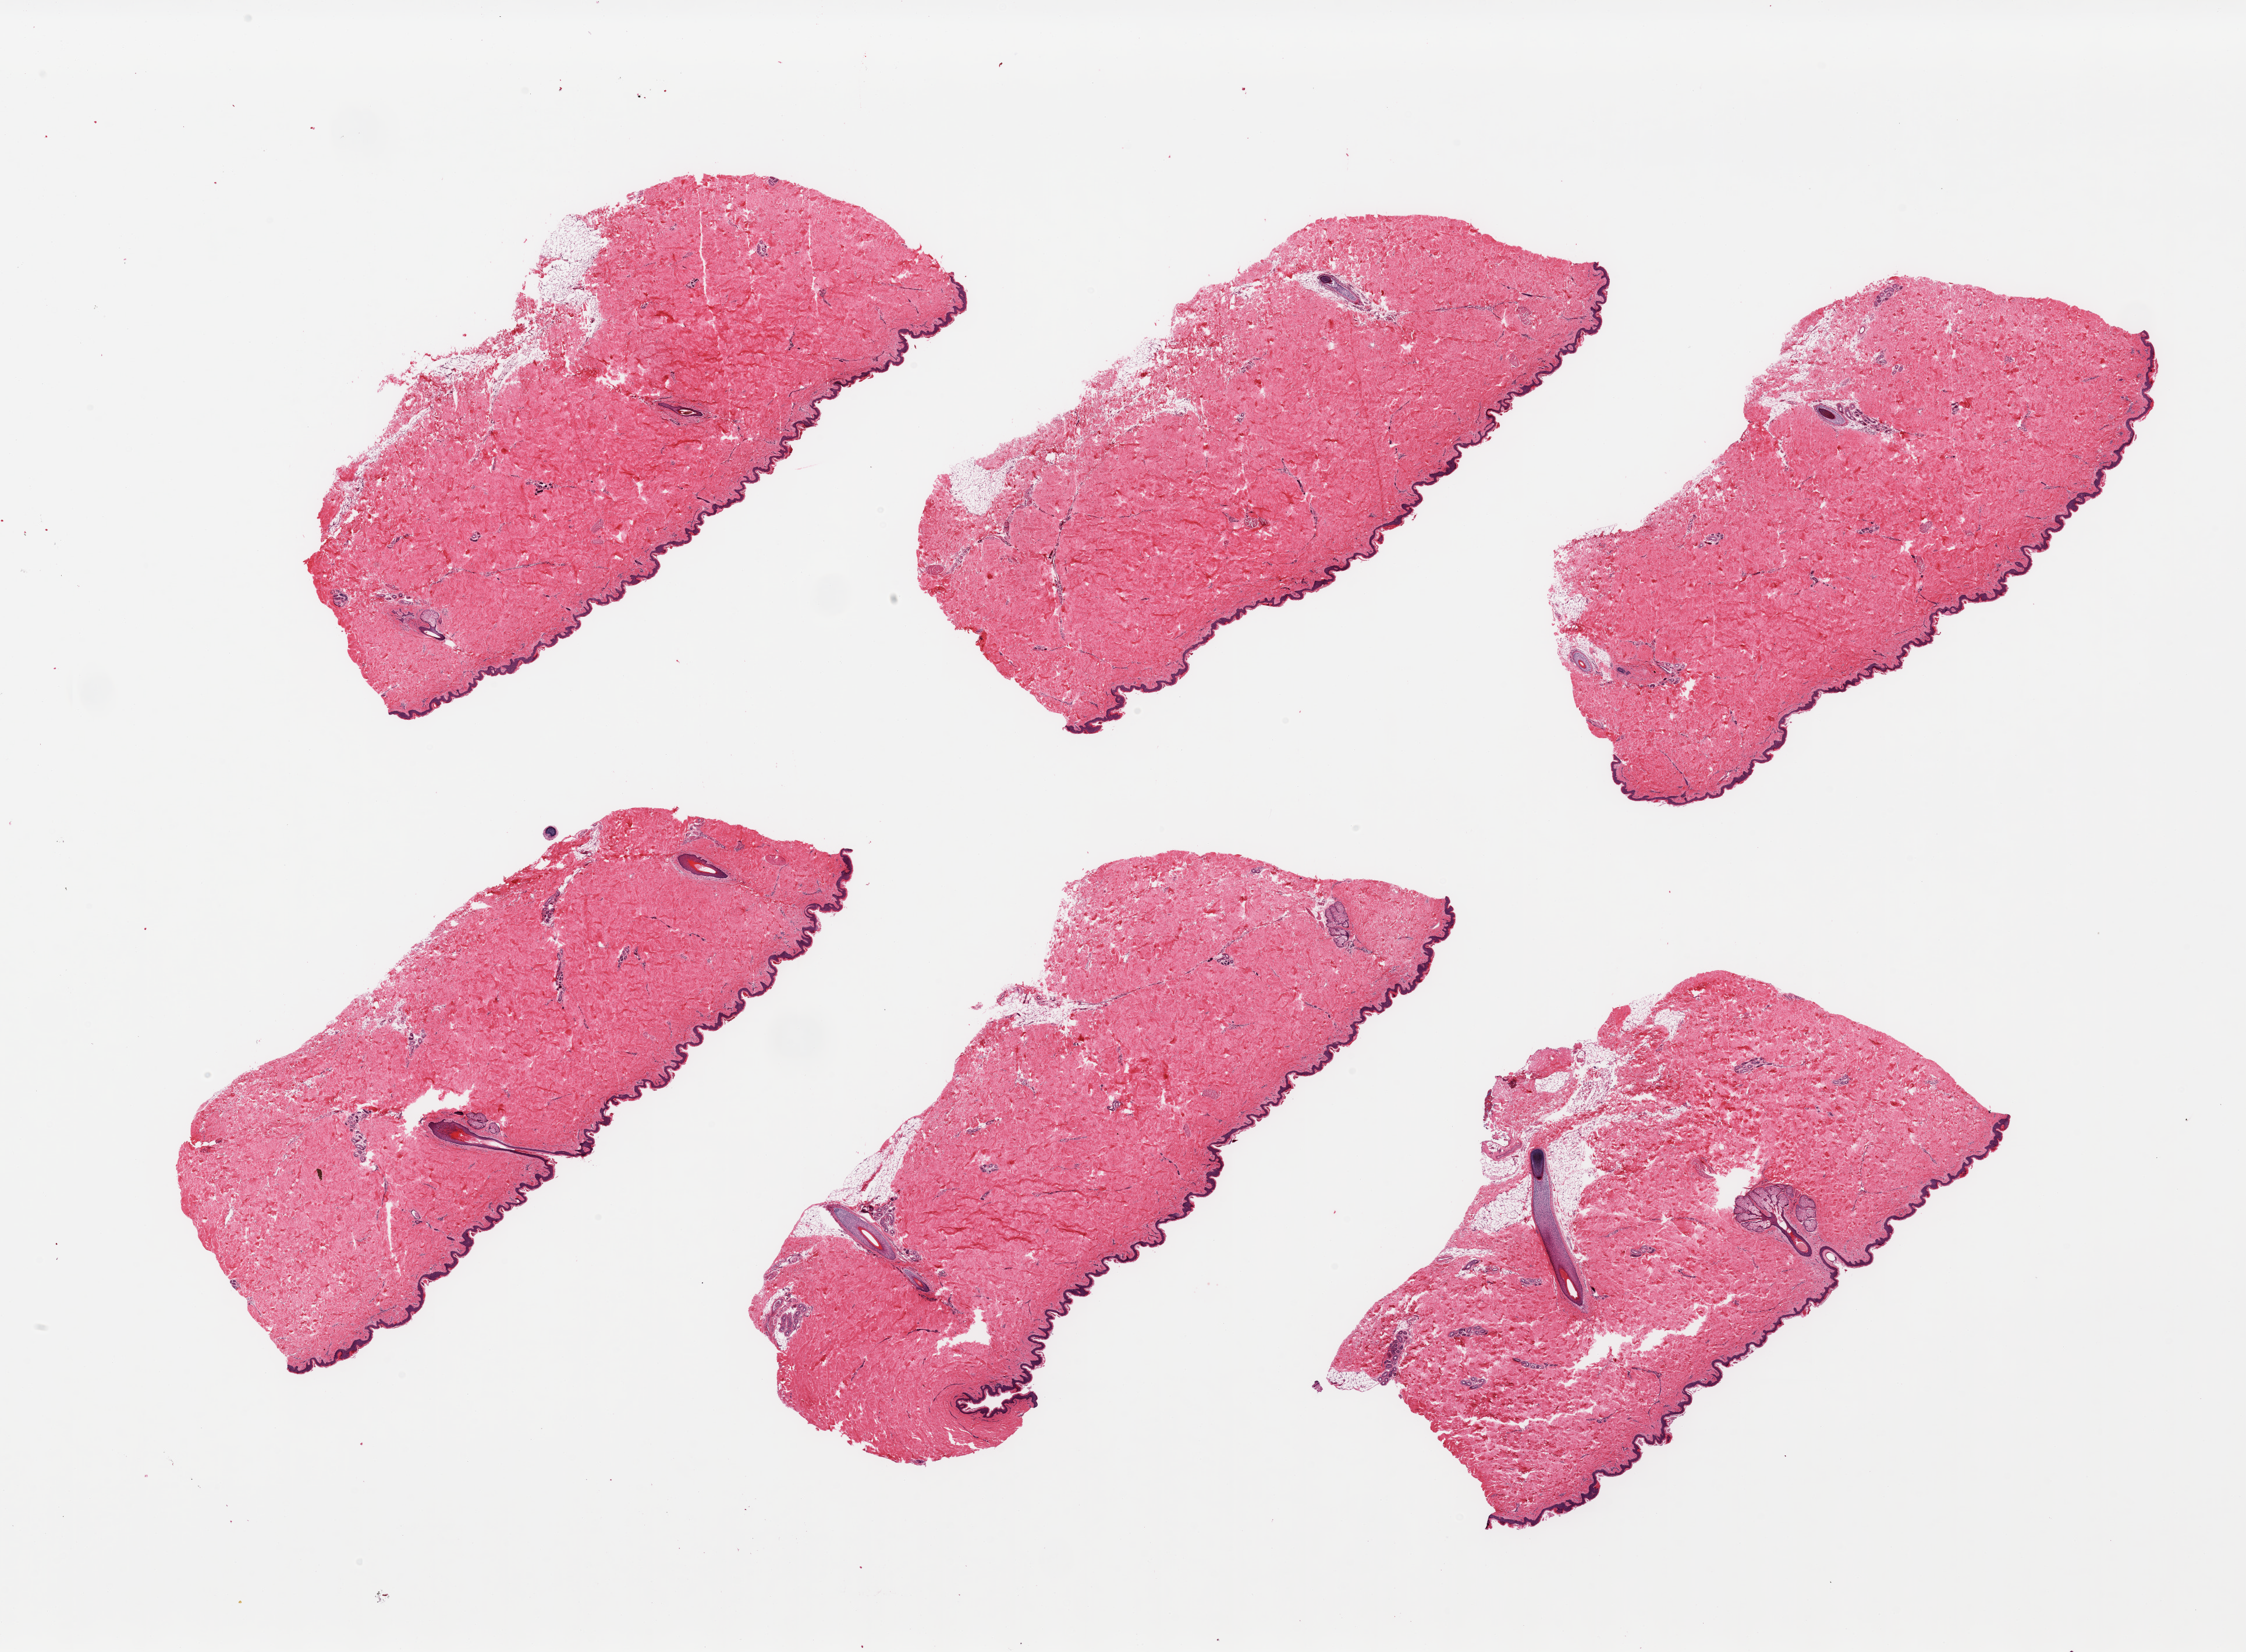
Digitized H&E-stained section, low-resolution overview of the scanned area, about 30.5 x 22.5 mm; PAXgene-fixed paraffin-embedded (PFPE) section; sampled site (target tissue): skin of suprapubic region; donor tissue sample. Donor sex: male.
* pathologist's review note for this sample: 6 pieces, trace dermal fat; squamous epithelium is ~45 microns